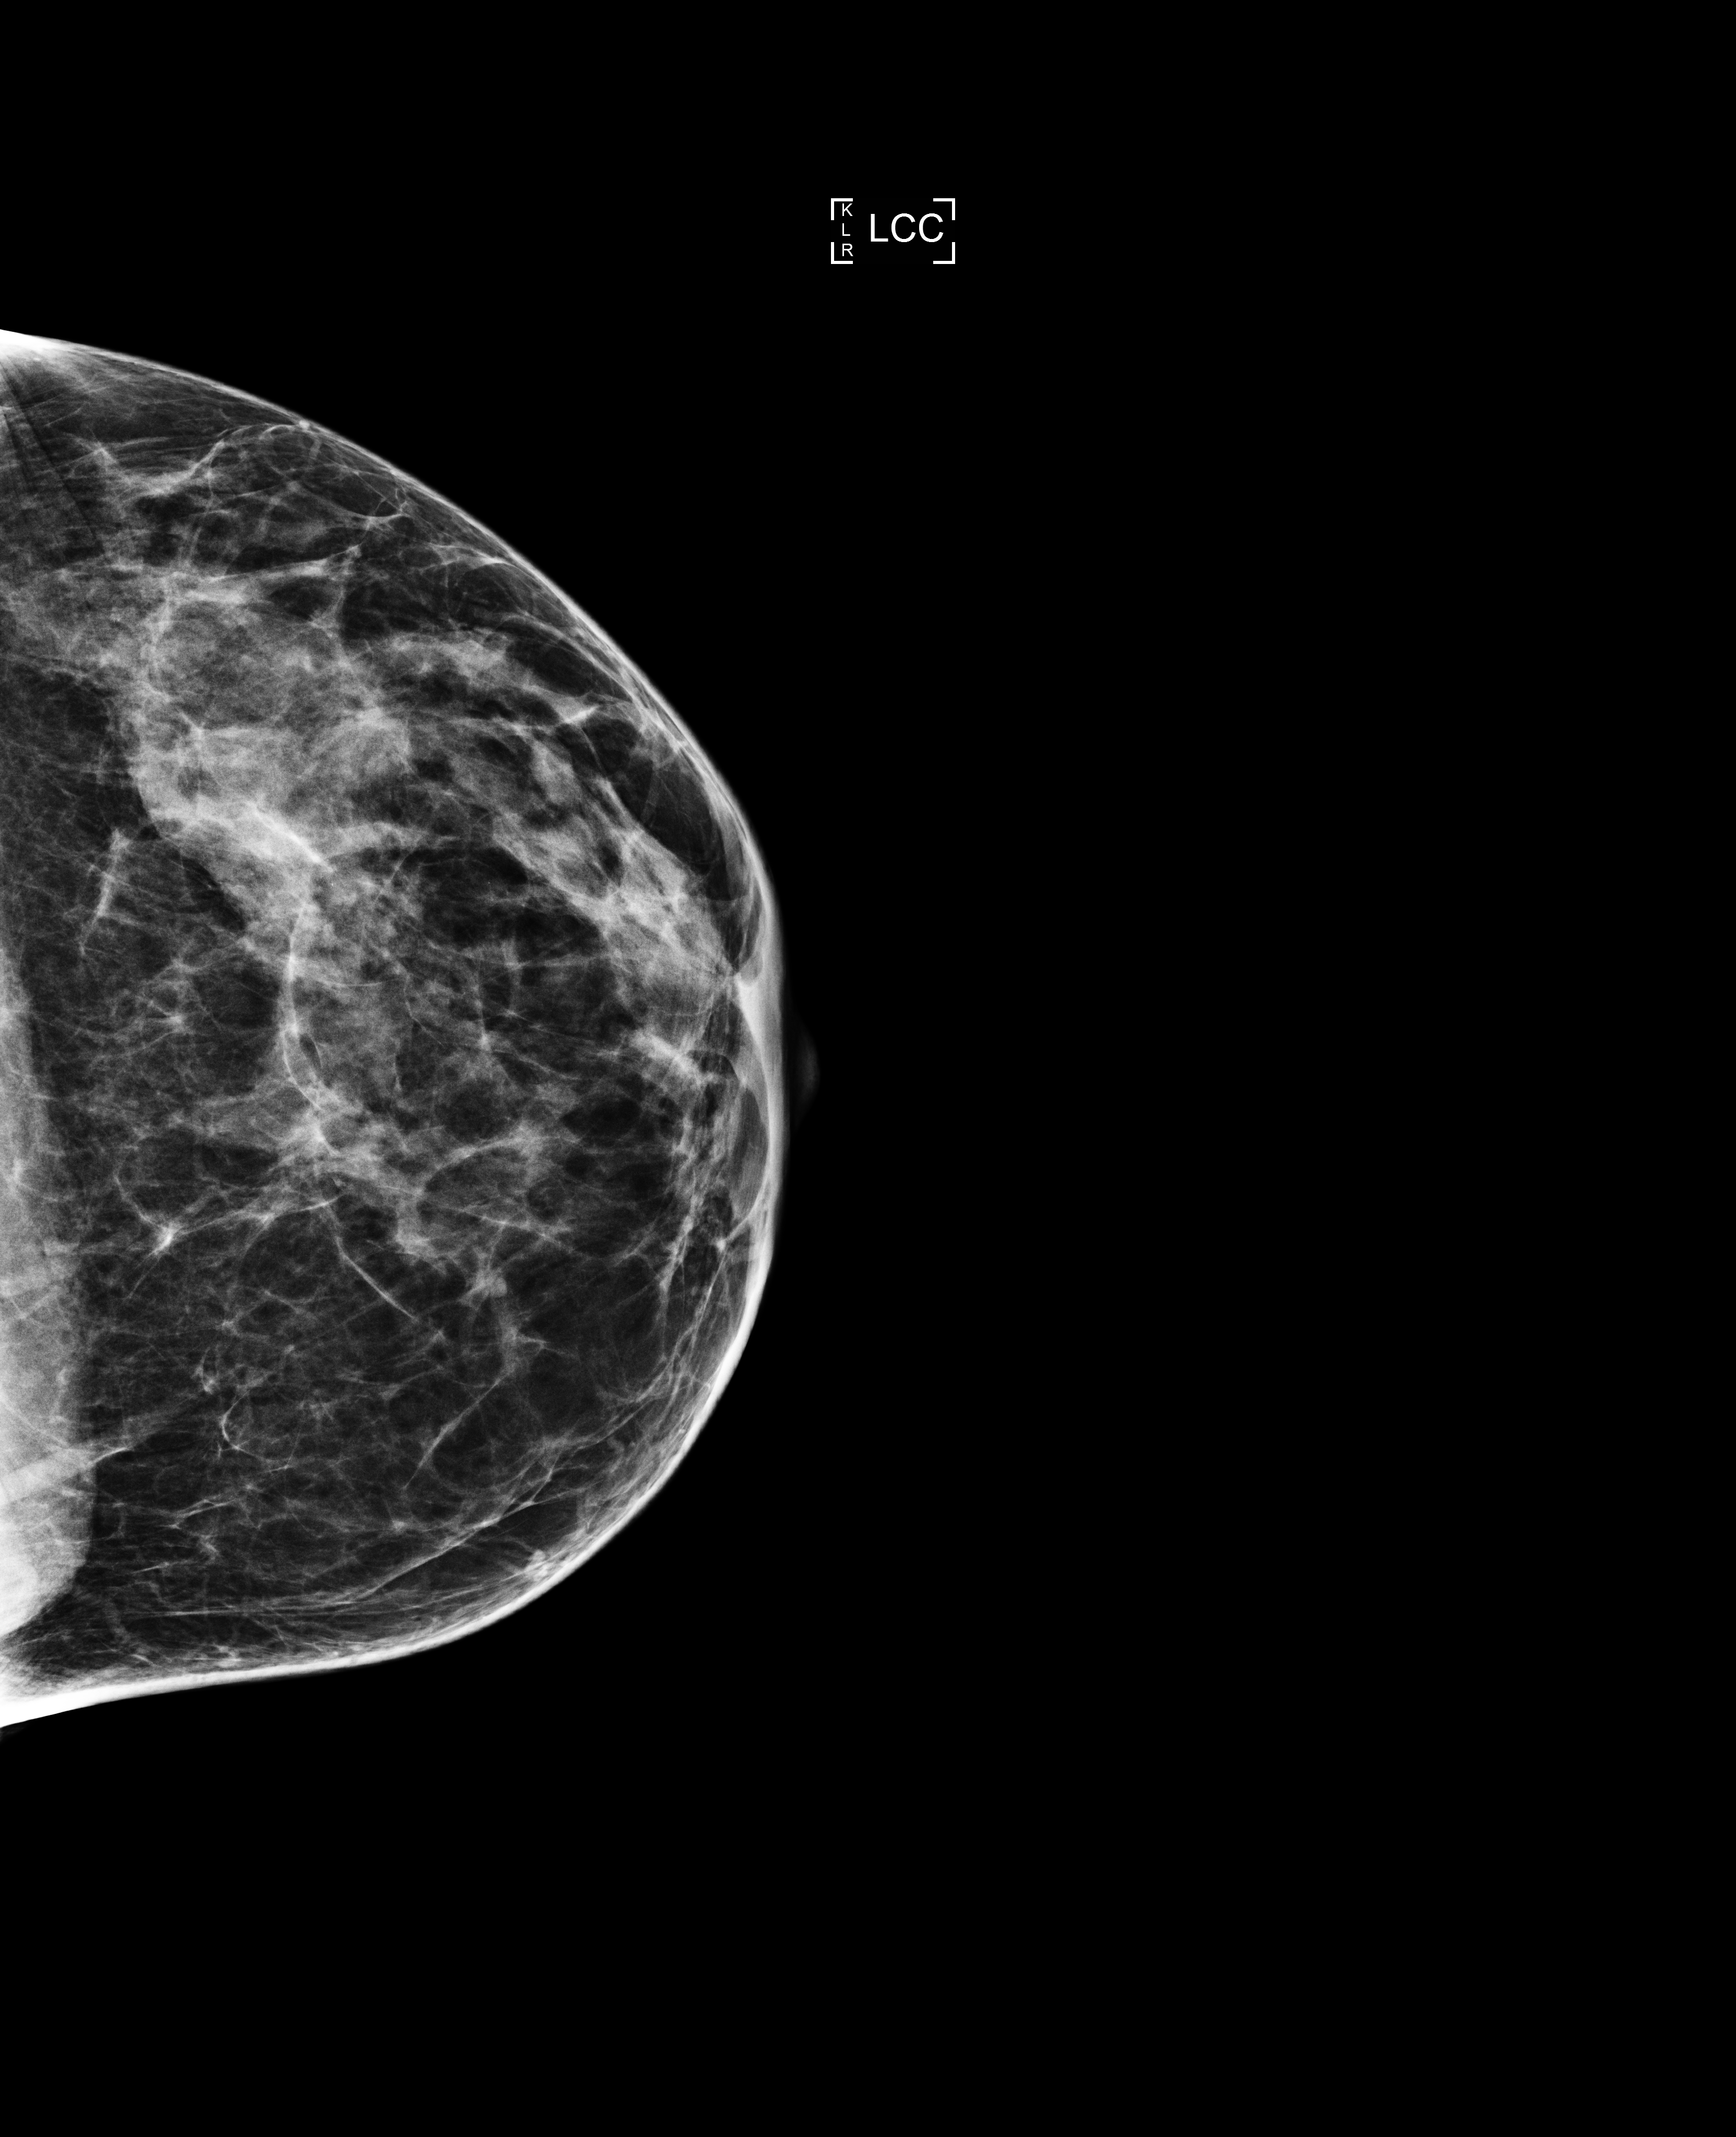
Screening examination; compressed breast thickness 47 mm; system: Selenia Dimensions. Patient aged 41 years (female).
Image type: full-field digital mammogram. Breast: left. Projection: cranio-caudal projection.